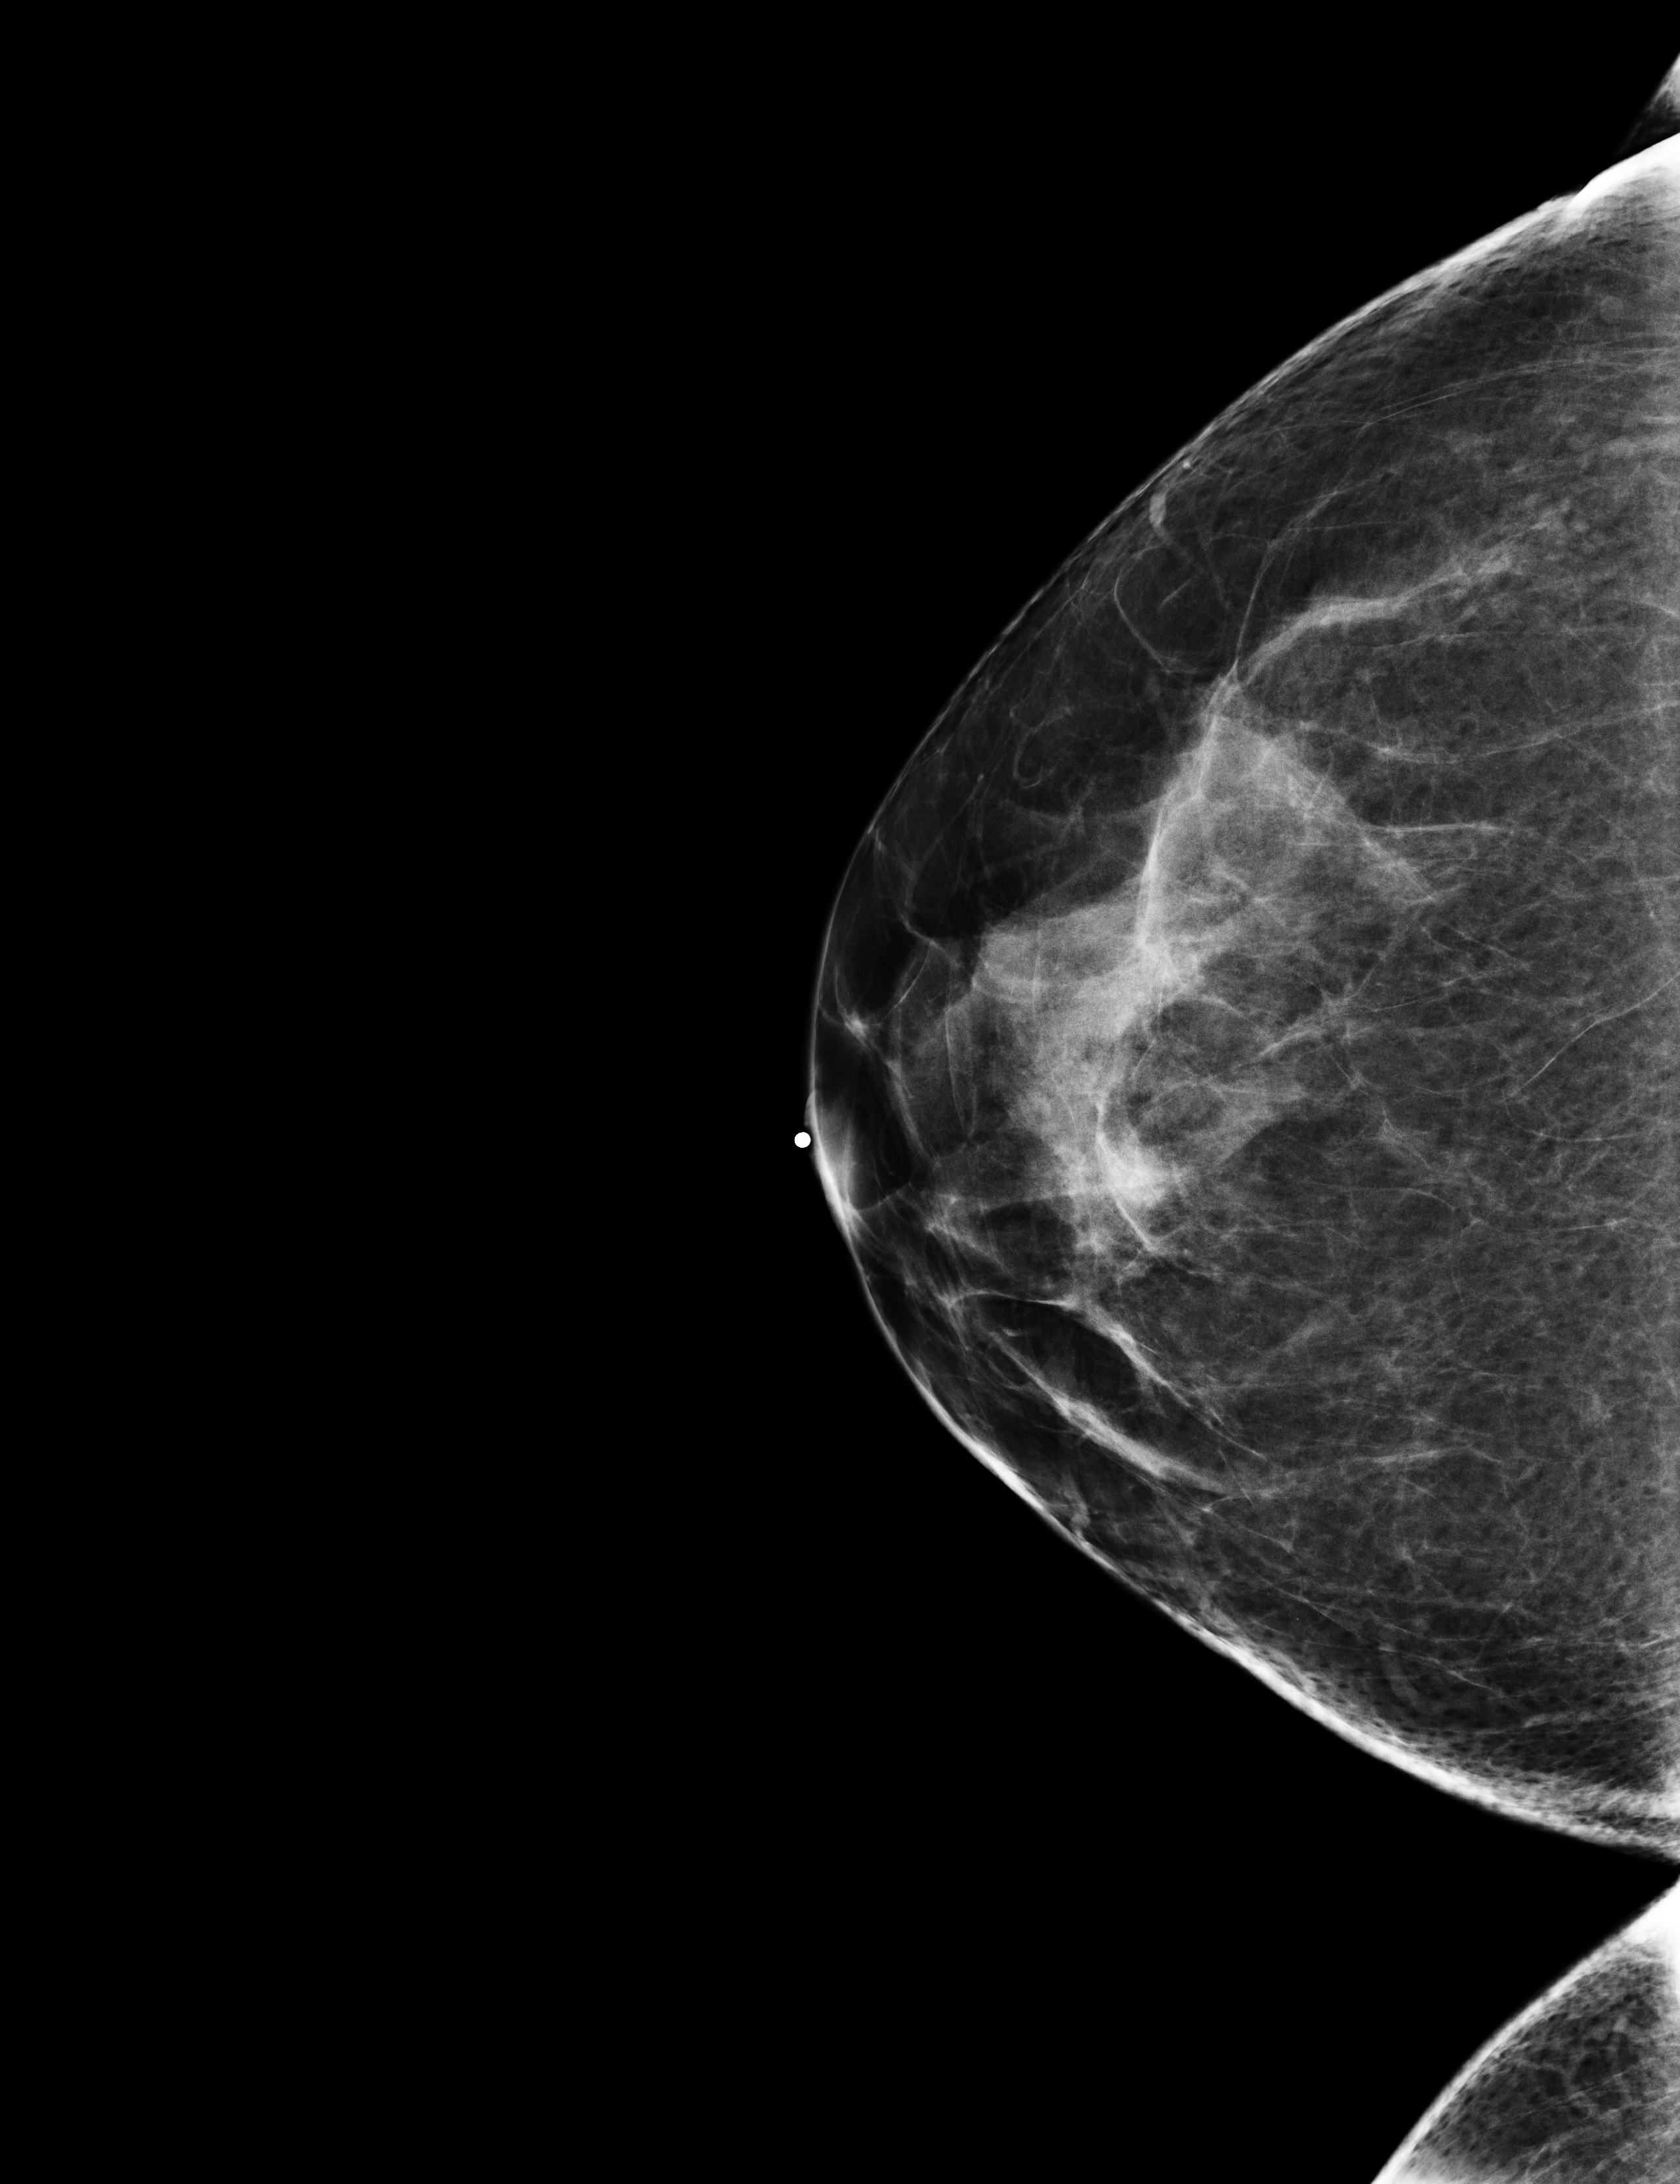
Annual screening mammography examination; compressed breast thickness 66 mm; system: Selenia Dimensions. Patient aged 50 years (female).
Image type: full-field digital mammogram. Breast: right. Projection: cranio-caudal projection.